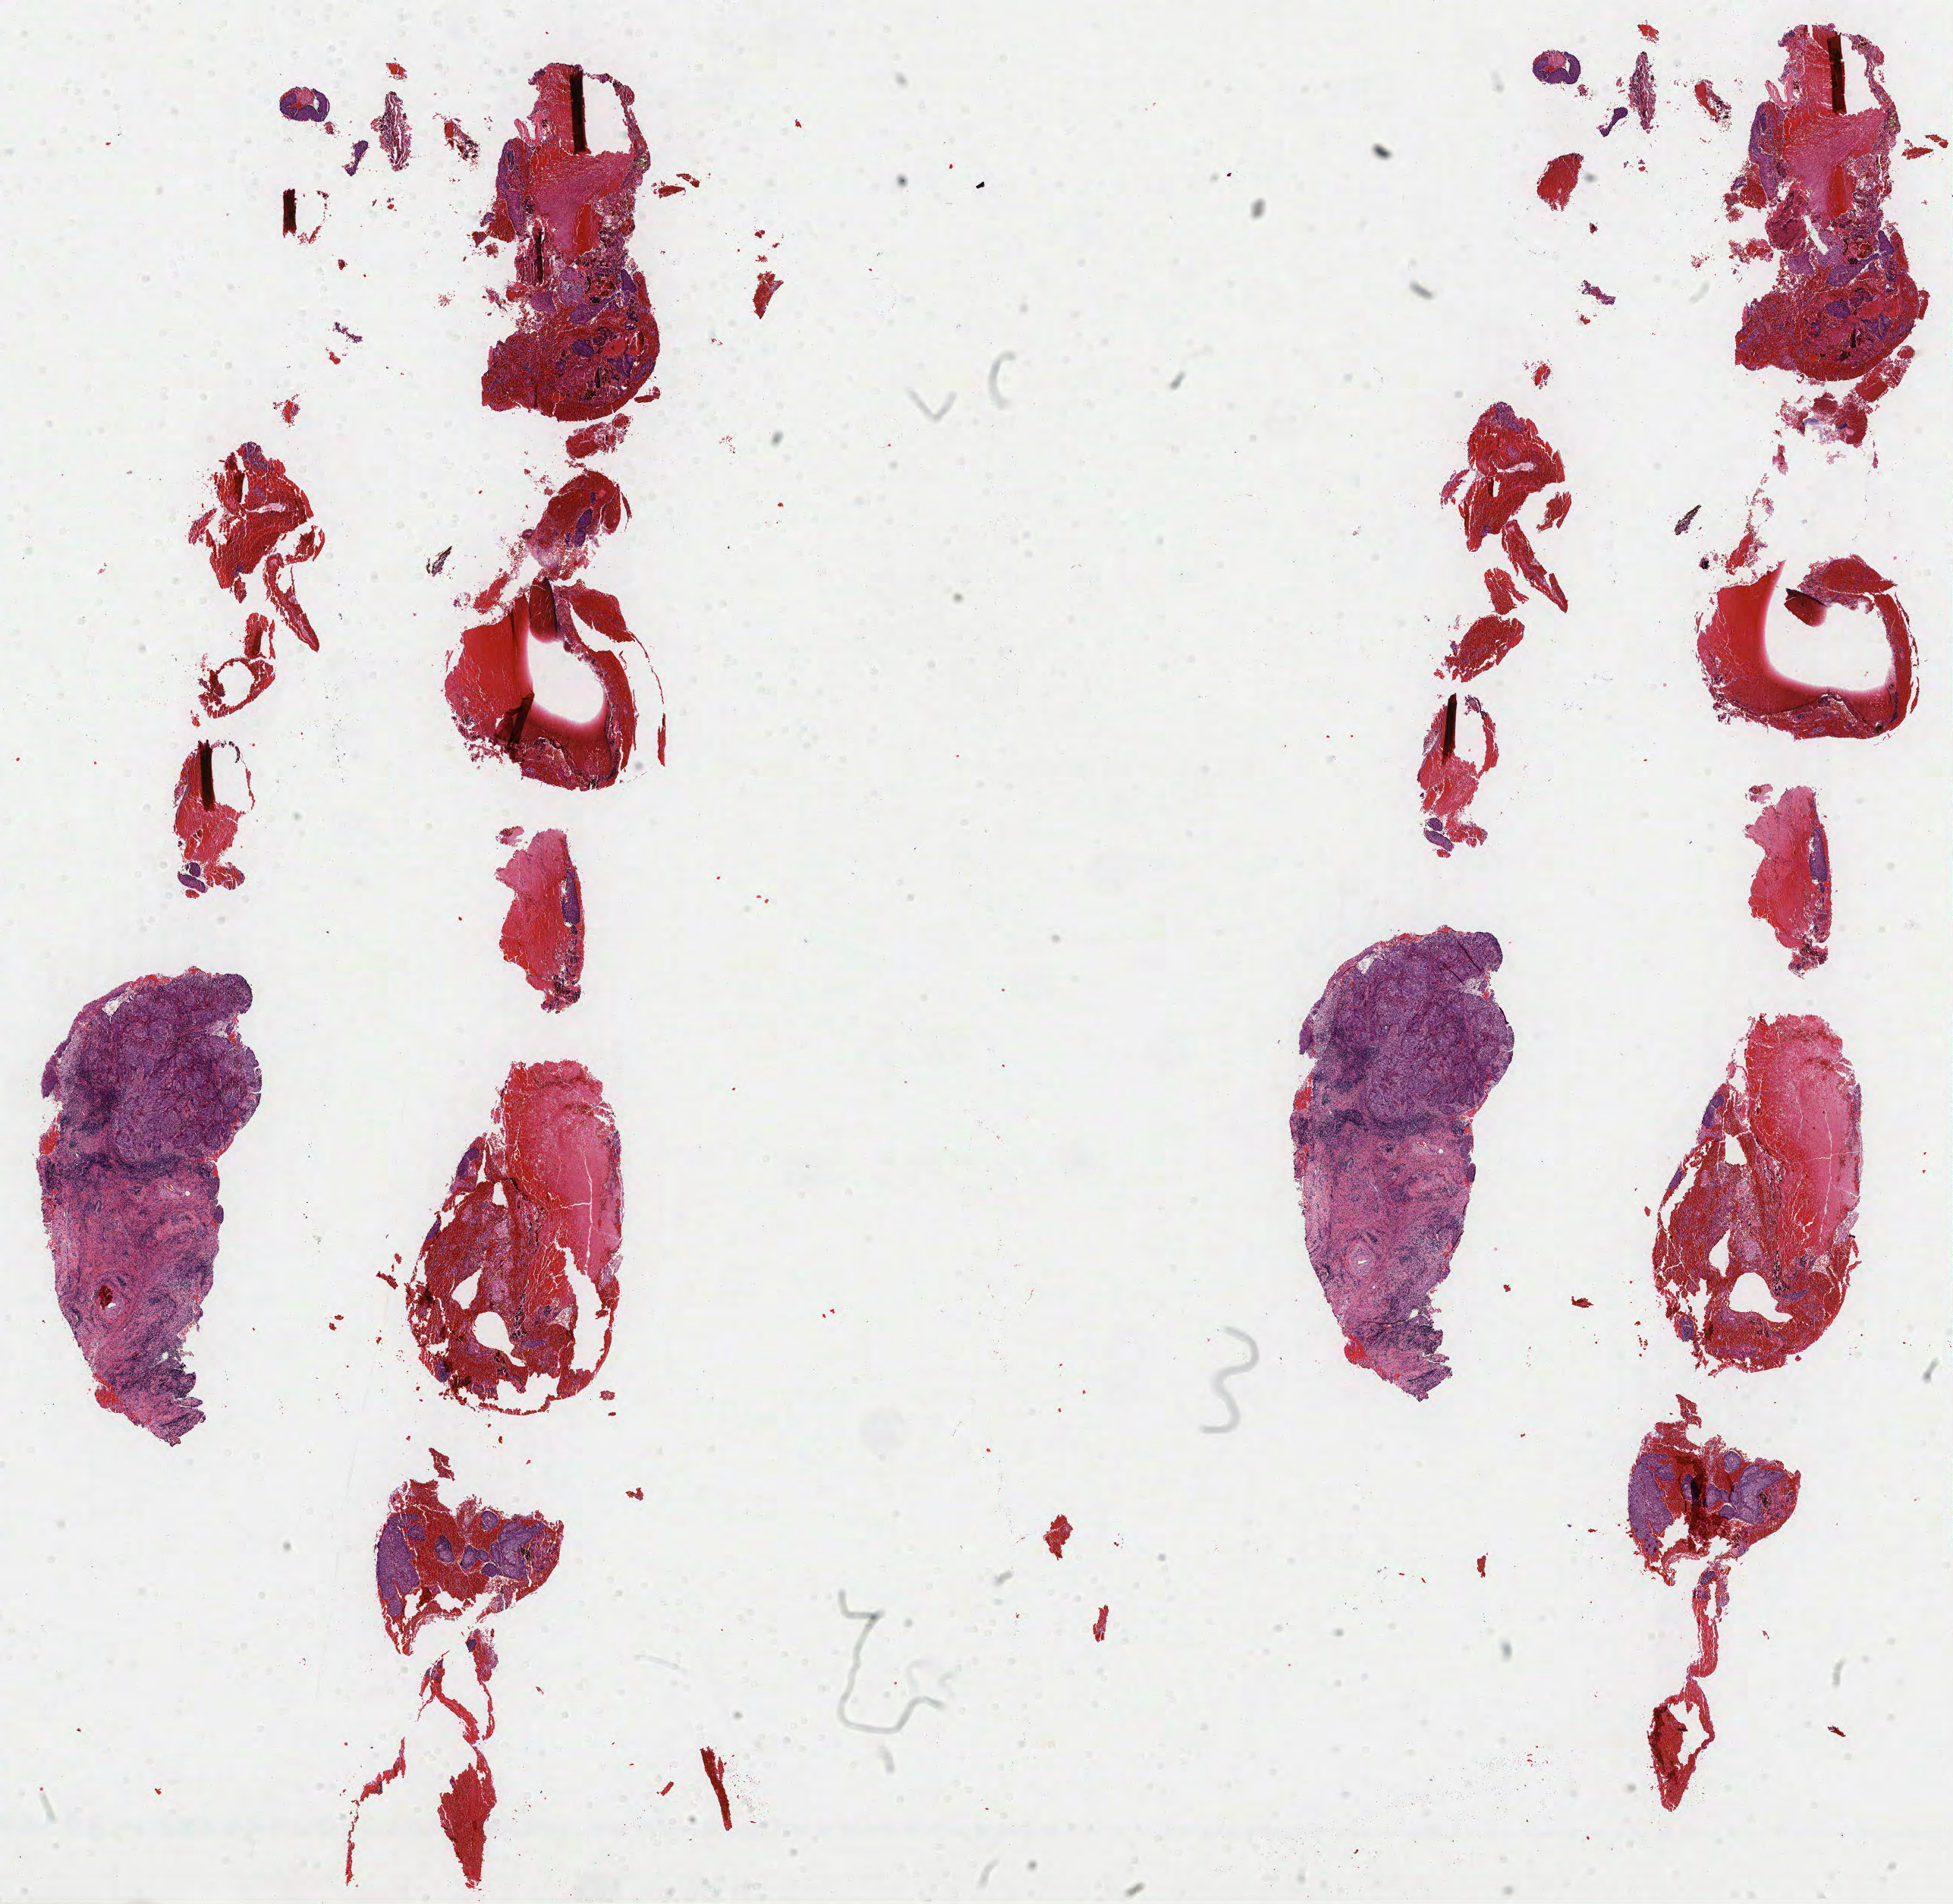
Hematoxylin and eosin (H&E) stained whole-slide image, shown as a low-resolution overview of the whole scanned area (about 20.7 x 20.2 mm, from a 40x scan). FFPE section. Sample: primary tumour, cervix. Female patient; age at initial diagnosis 58 years. Histologic grade: G2 (moderately differentiated).
• FIGO stage: IIIB
• diagnosis: Squamous cell carcinoma, large cell, nonkeratinizing, NOS (cervix uteri)